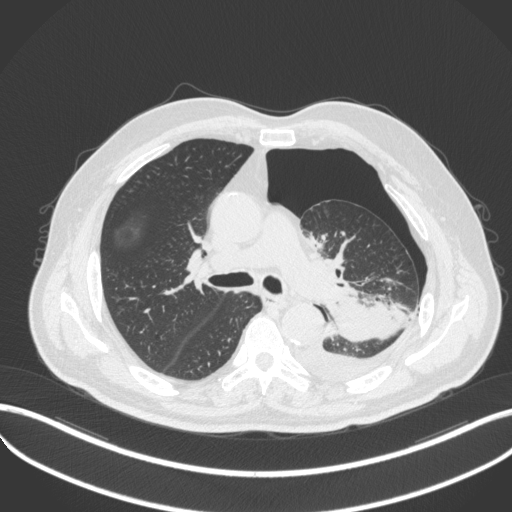
Chest CT, one axial slice. Slice 322 of 466 in the series (ordered by position). Lung window (W 1500 / L -600 HU). 512 × 512 image matrix, field of view 400 × 400 mm. Male patient, age 76 years. From the clinical record (not read from this slice): clinical TNM (as recorded): T3 N0 M1b.
Outlined on this slice (rectangle marked by the reading radiologist):
- lung tumour (recorded histology: adenocarcinoma): bounding box <325,295,405,349> (left, top, right, bottom; pixels)